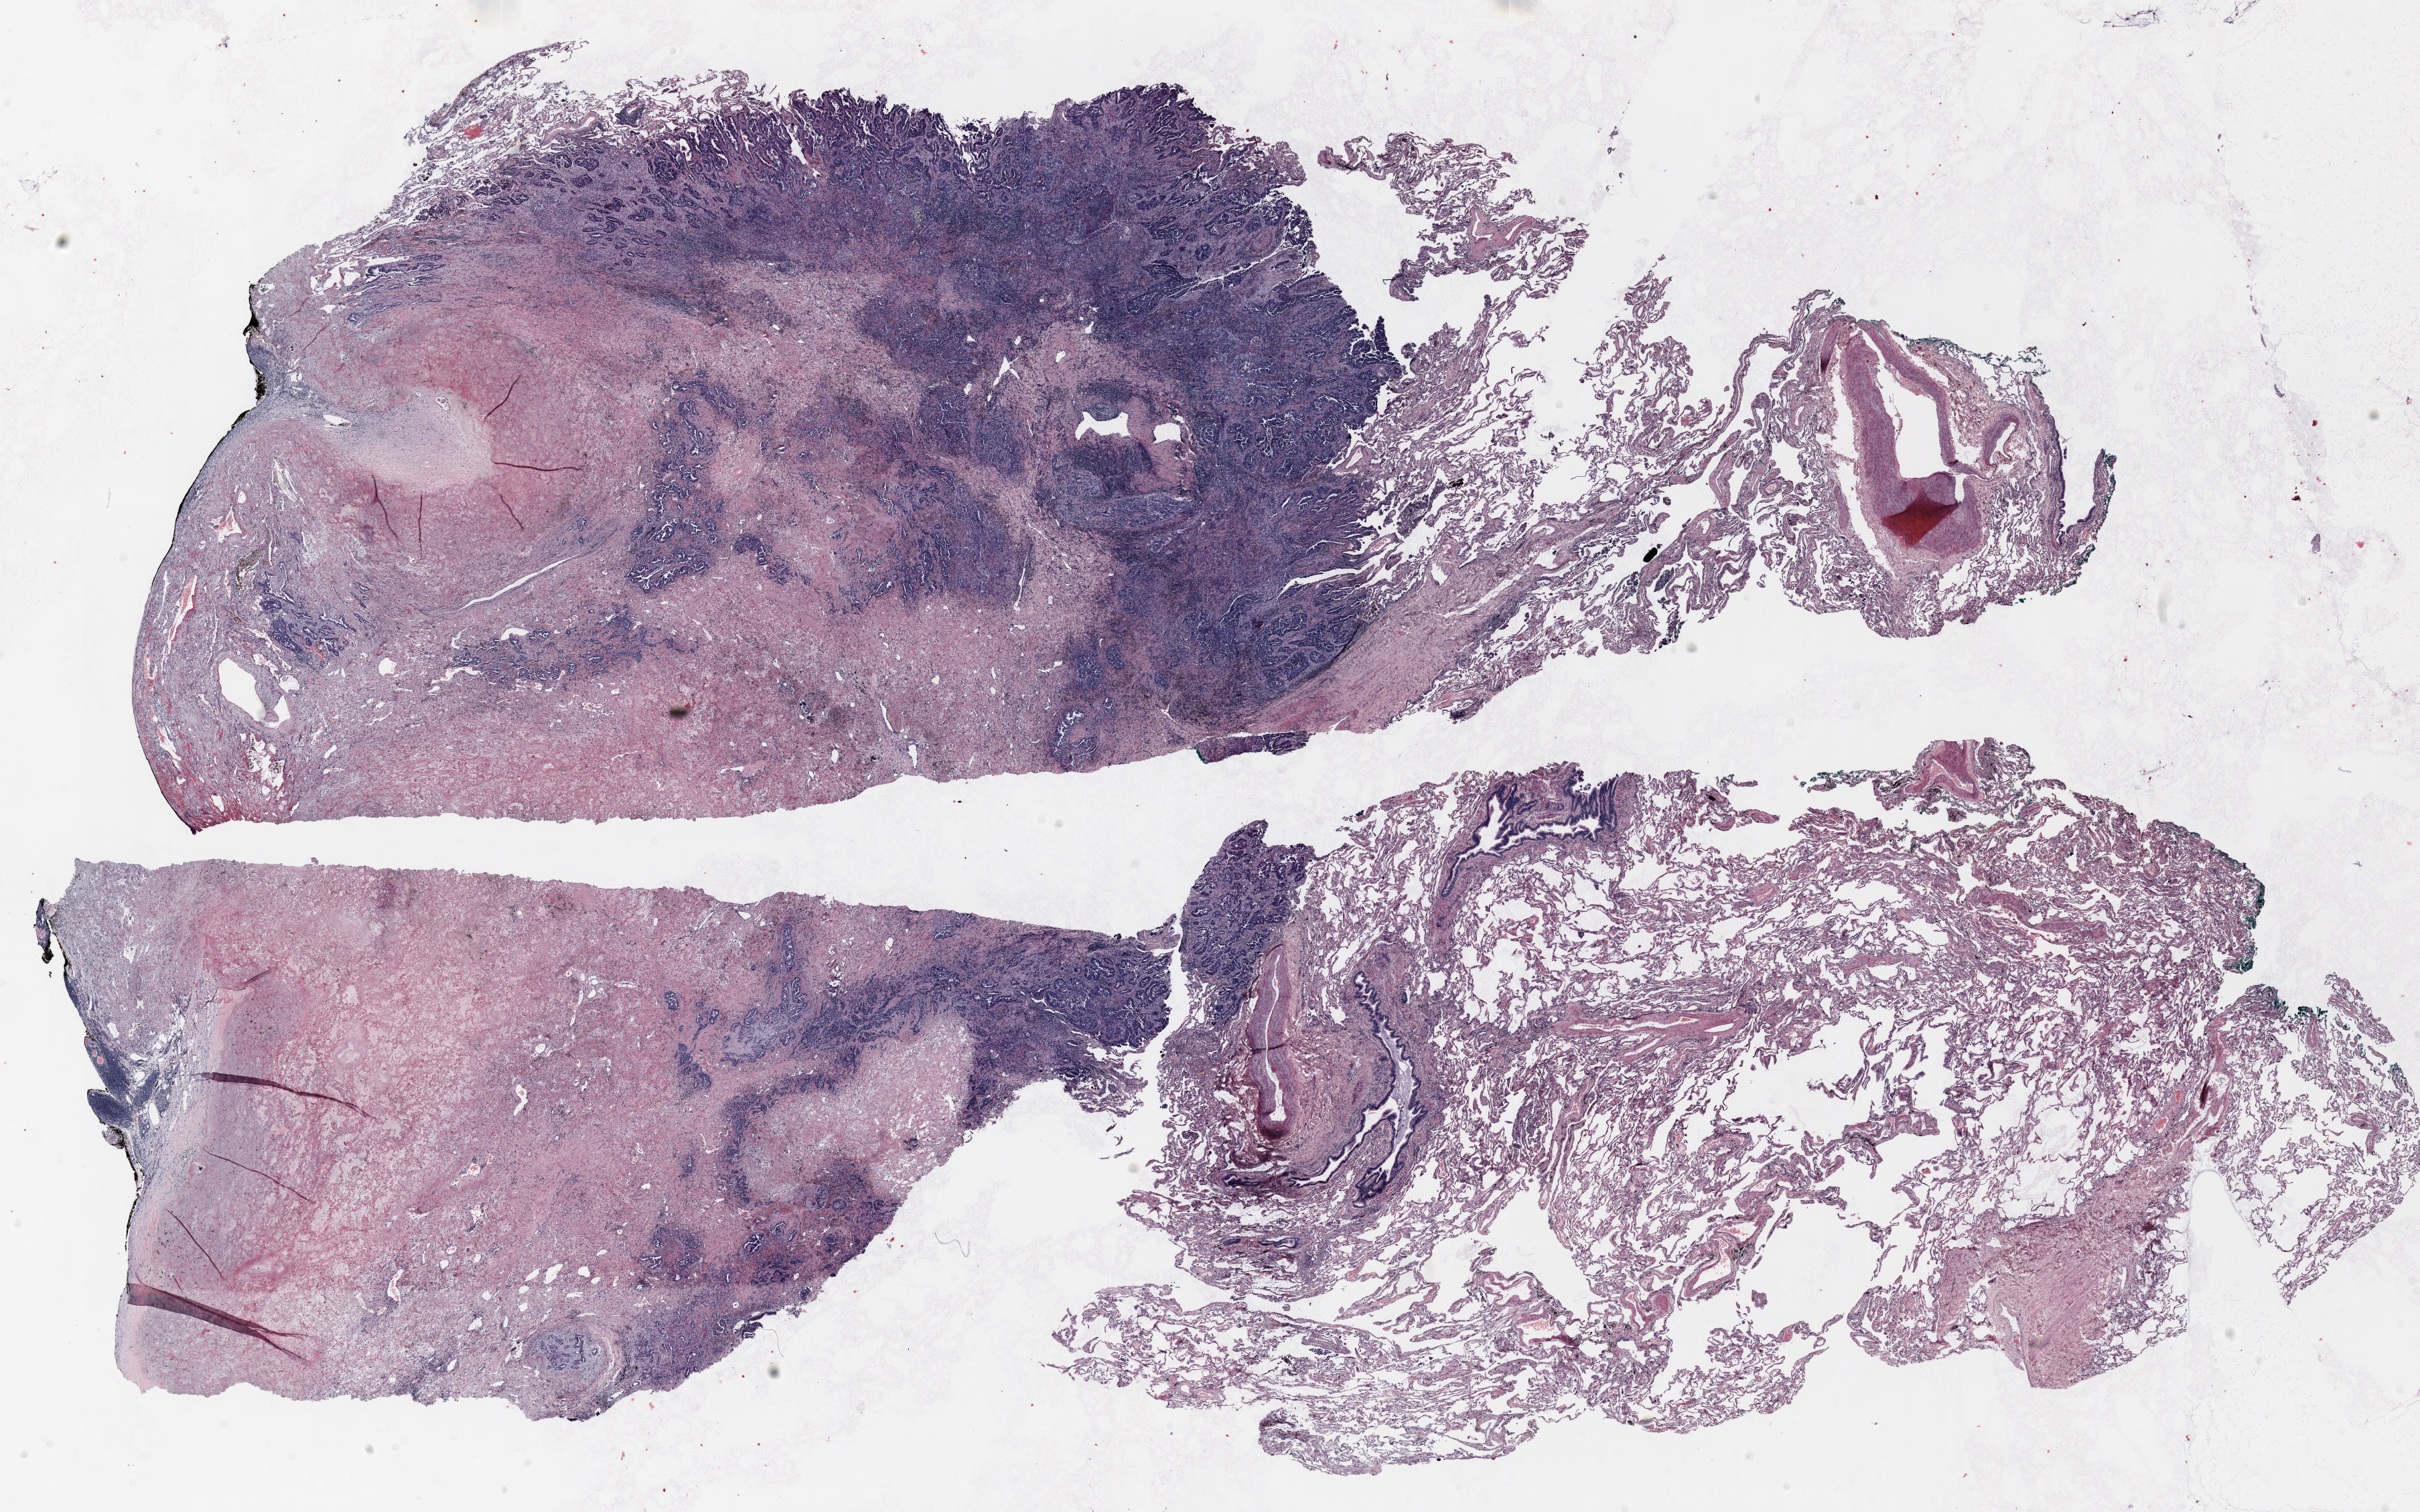
Whole-slide histology image, Hematoxylin and eosin (H&E) stained — whole scanned area (about 29.0 x 18.1 mm, acquisition: 20x scan) shown as a low-resolution overview. FFPE section. Lung. Female, age 66 at enrolment. Former smoker at enrolment.
Participant's lung-cancer diagnosis: Adenocarcinoma, NOS.